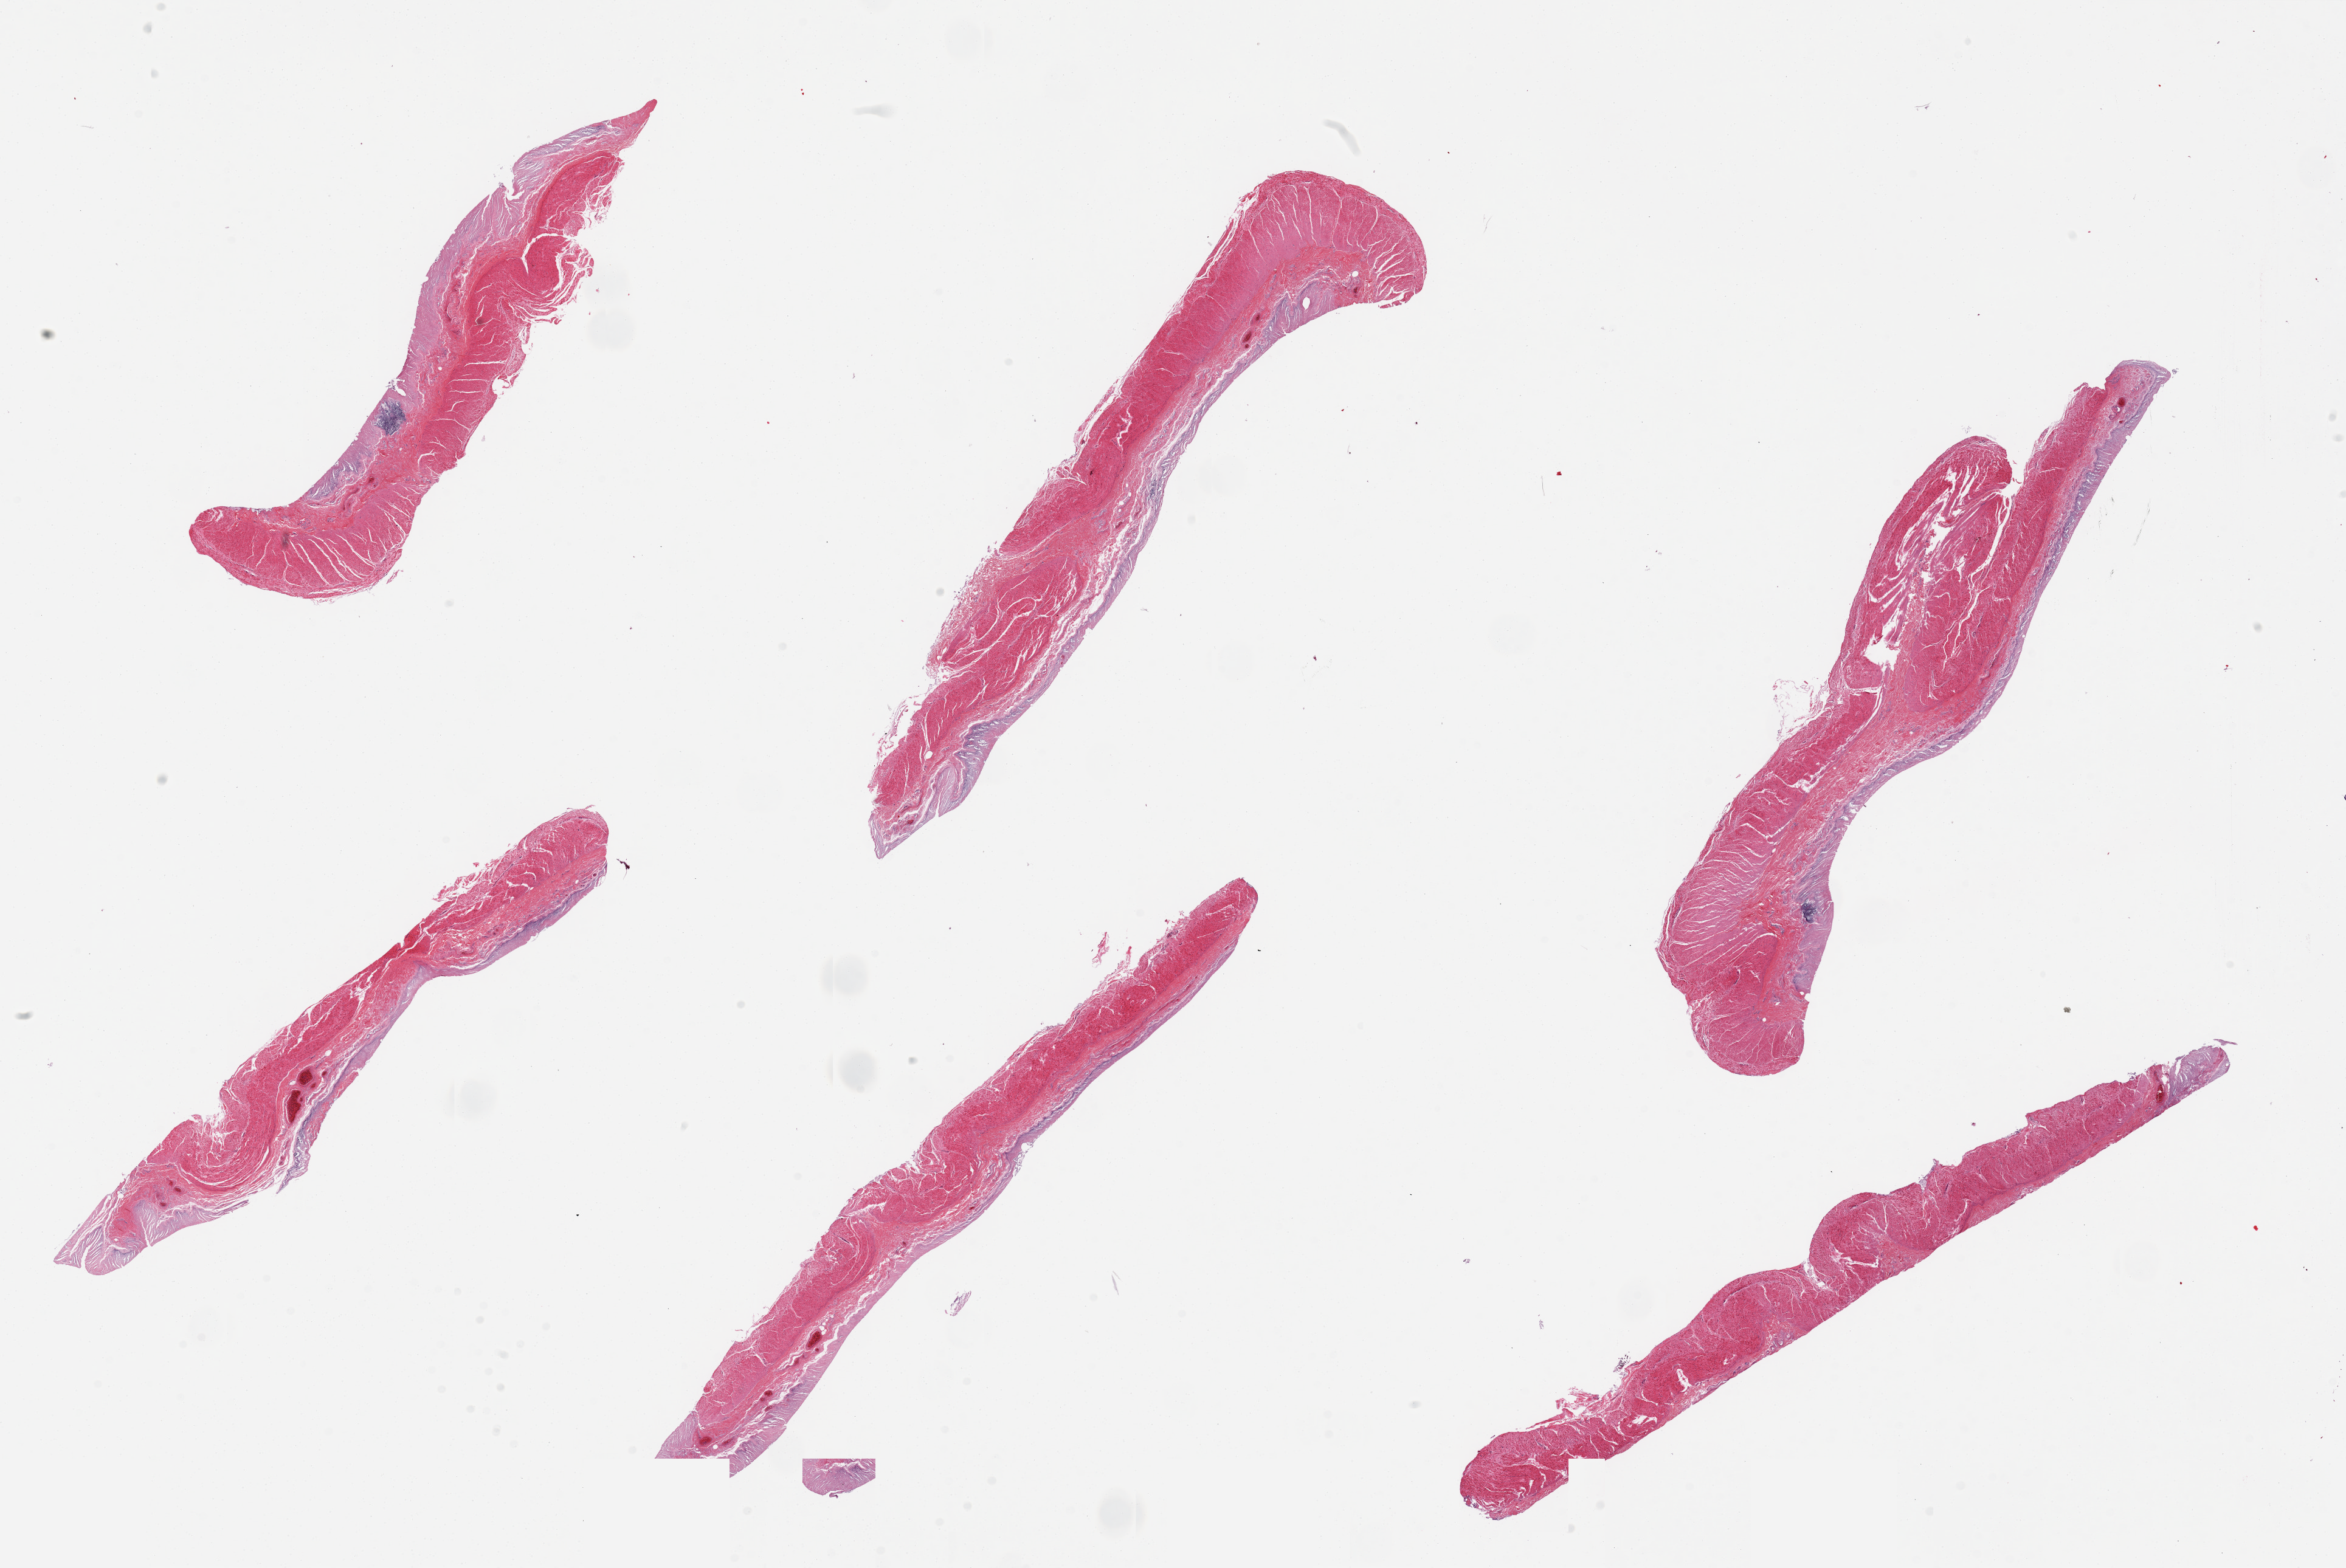
Haematoxylin and eosin whole-slide image, brightfield — whole scanned area (about 30.5 x 20.4 mm, slide scanned at 20x) shown as a low-resolution overview, PAXgene-fixed paraffin-embedded (PFPE) section, section of transverse colon (target tissue), donor tissue sample. Donor sex: male.
Pathologist's review note for this sample: 6 pieces, mucosa totally autolyzed, ~0.1mm thick.